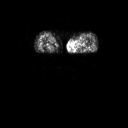
FDG PET of an extremity soft-tissue mass (from a PET/CT study), one axial slice; position 4 of 91 along the scan axis; 3.27 mm slice thickness; 128 × 128 image matrix. Patient: female, 74 years. Case-level facts recorded for this patient, not image findings: histological type: pleomorphic leiomyosarcoma; grade: high; site of the primary tumour: left thigh.
Annotated regions visible in this slice (expert contour drawn on MRI and transferred to this co-registered scan by the dataset authors):
- gross tumour volume including surrounding oedema: box from (x=72, y=37) to (x=87, y=51) px